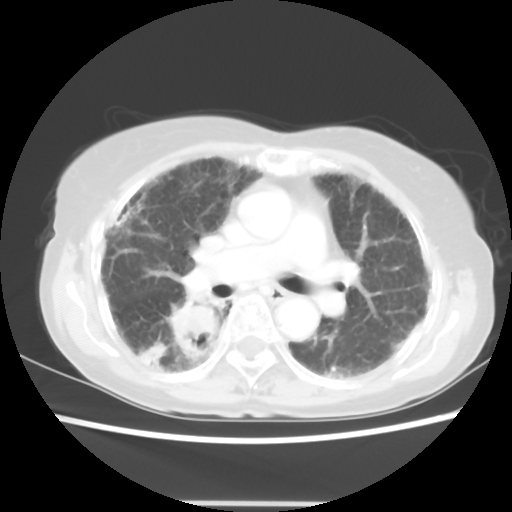
Chest CT, one axial slice. Position 31 of 52 along the scan axis. 120 kVp. Lung window (W 1500 / L -600 HU). 5 mm slice thickness. 512 × 512 image matrix. Patient: female, 71 years. Case-level facts recorded for this patient, not image findings: clinical TNM (as recorded): T3 N0 M0.
Structures marked on this image (bounding box drawn by a radiologist):
- lung tumour (recorded histology: squamous cell carcinoma): bounding box [x1, y1, x2, y2] px = [166, 296, 221, 359]